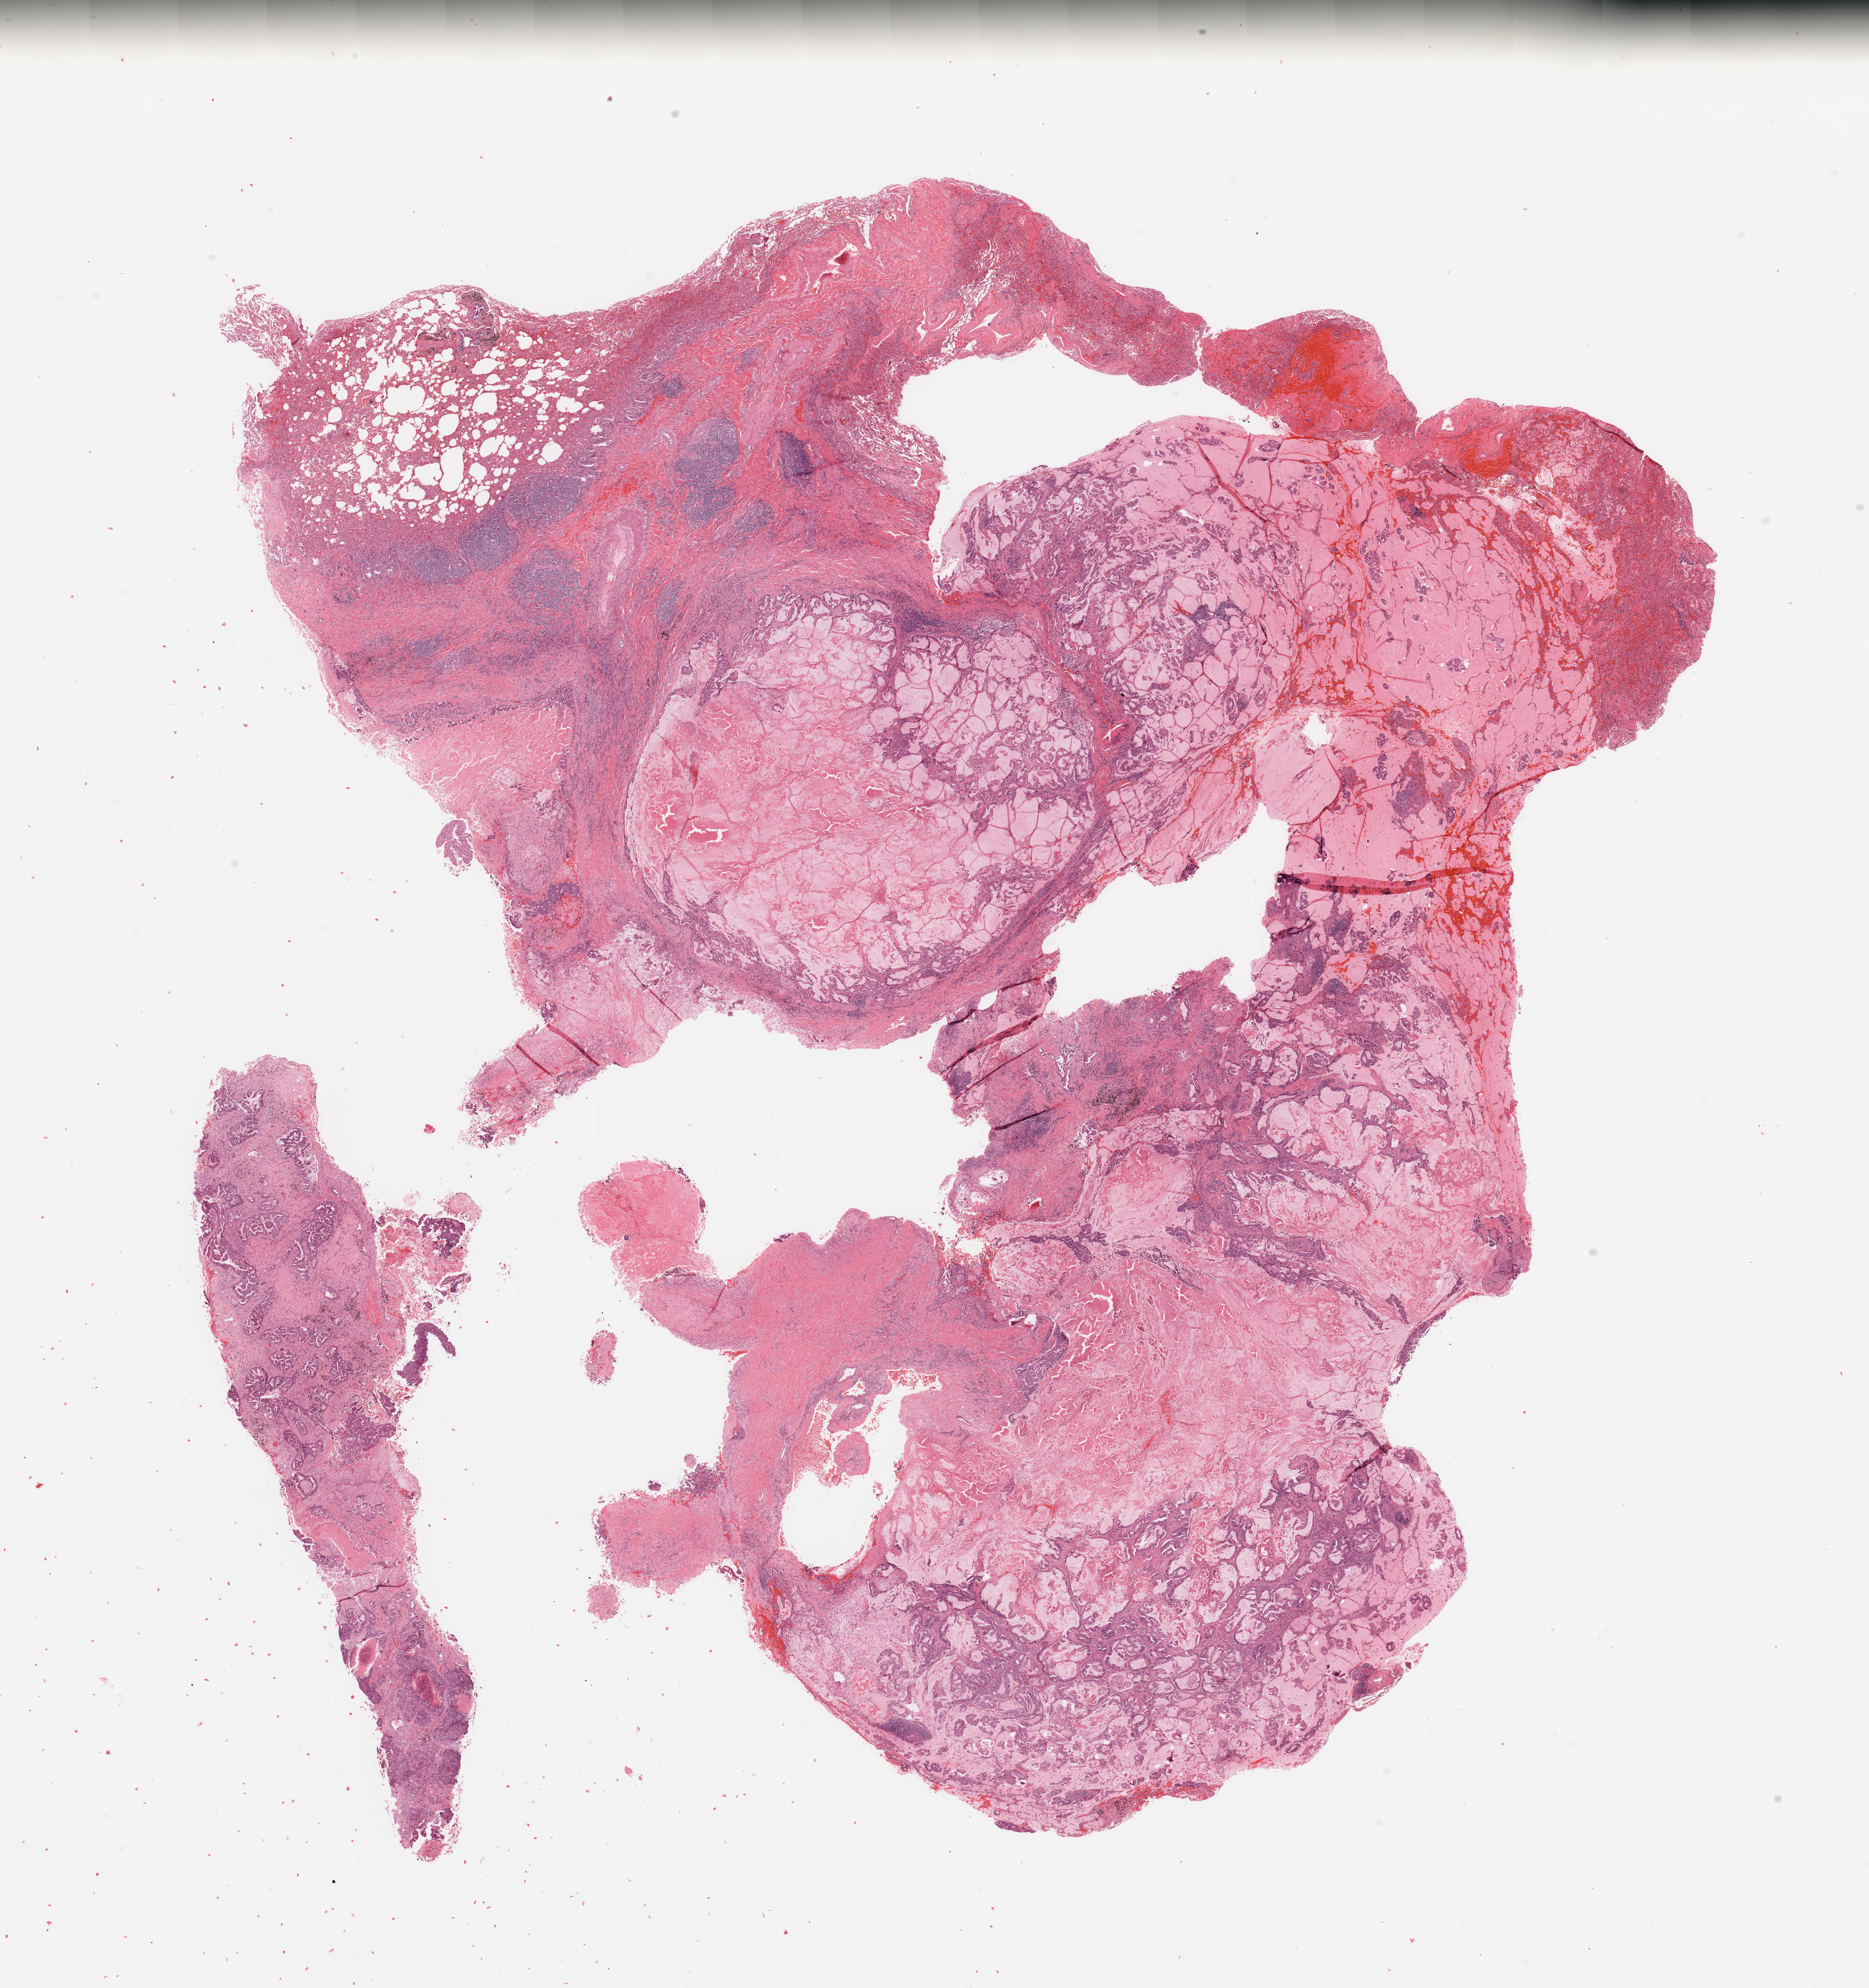
Hematoxylin and eosin (H&E) stained whole-slide image — low-resolution overview of the scanned area, about 20.7 x 22.0 mm, lung, tumour tissue. Male, 40 y/o. Histologic grade: G2 (moderately differentiated).
Primary tumour site (as recorded): right lower lobe. Histologic diagnosis: Adenocarcinoma, NOS. AJCC pathologic stage: IB.